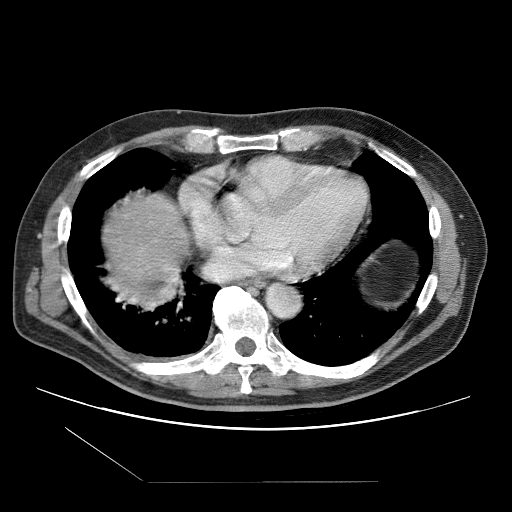
Contrast-enhanced abdominal CT (liver protocol), one axial slice. Position 101 of 109 along the scan axis. Reconstruction kernel STANDARD. One of 2 acquisitions stored at this slice position. Soft-tissue window (W 400 / L 40 HU). 2.5 mm slice thickness. 512 × 512 image matrix, field of view 400 × 400 mm. Case-level facts recorded for this patient, not image findings: diagnosis: hepatocellular carcinoma (patient treated with transarterial chemoembolisation; whether this scan precedes or follows treatment is not stated here); TNM stage (as recorded): Stage-IIIB; Child-Pugh class: A; tumour nodularity: multinodular.
Outlined on this slice (semi-automatically segmented with operator editing):
- liver parenchyma outside the tumour (the mass and vessels are separate outlines, so this box may not span the whole liver): bounding box (x1, y1, x2, y2) in pixels: (104, 194, 188, 286)
- liver vessels: (170, 268, 176, 282)